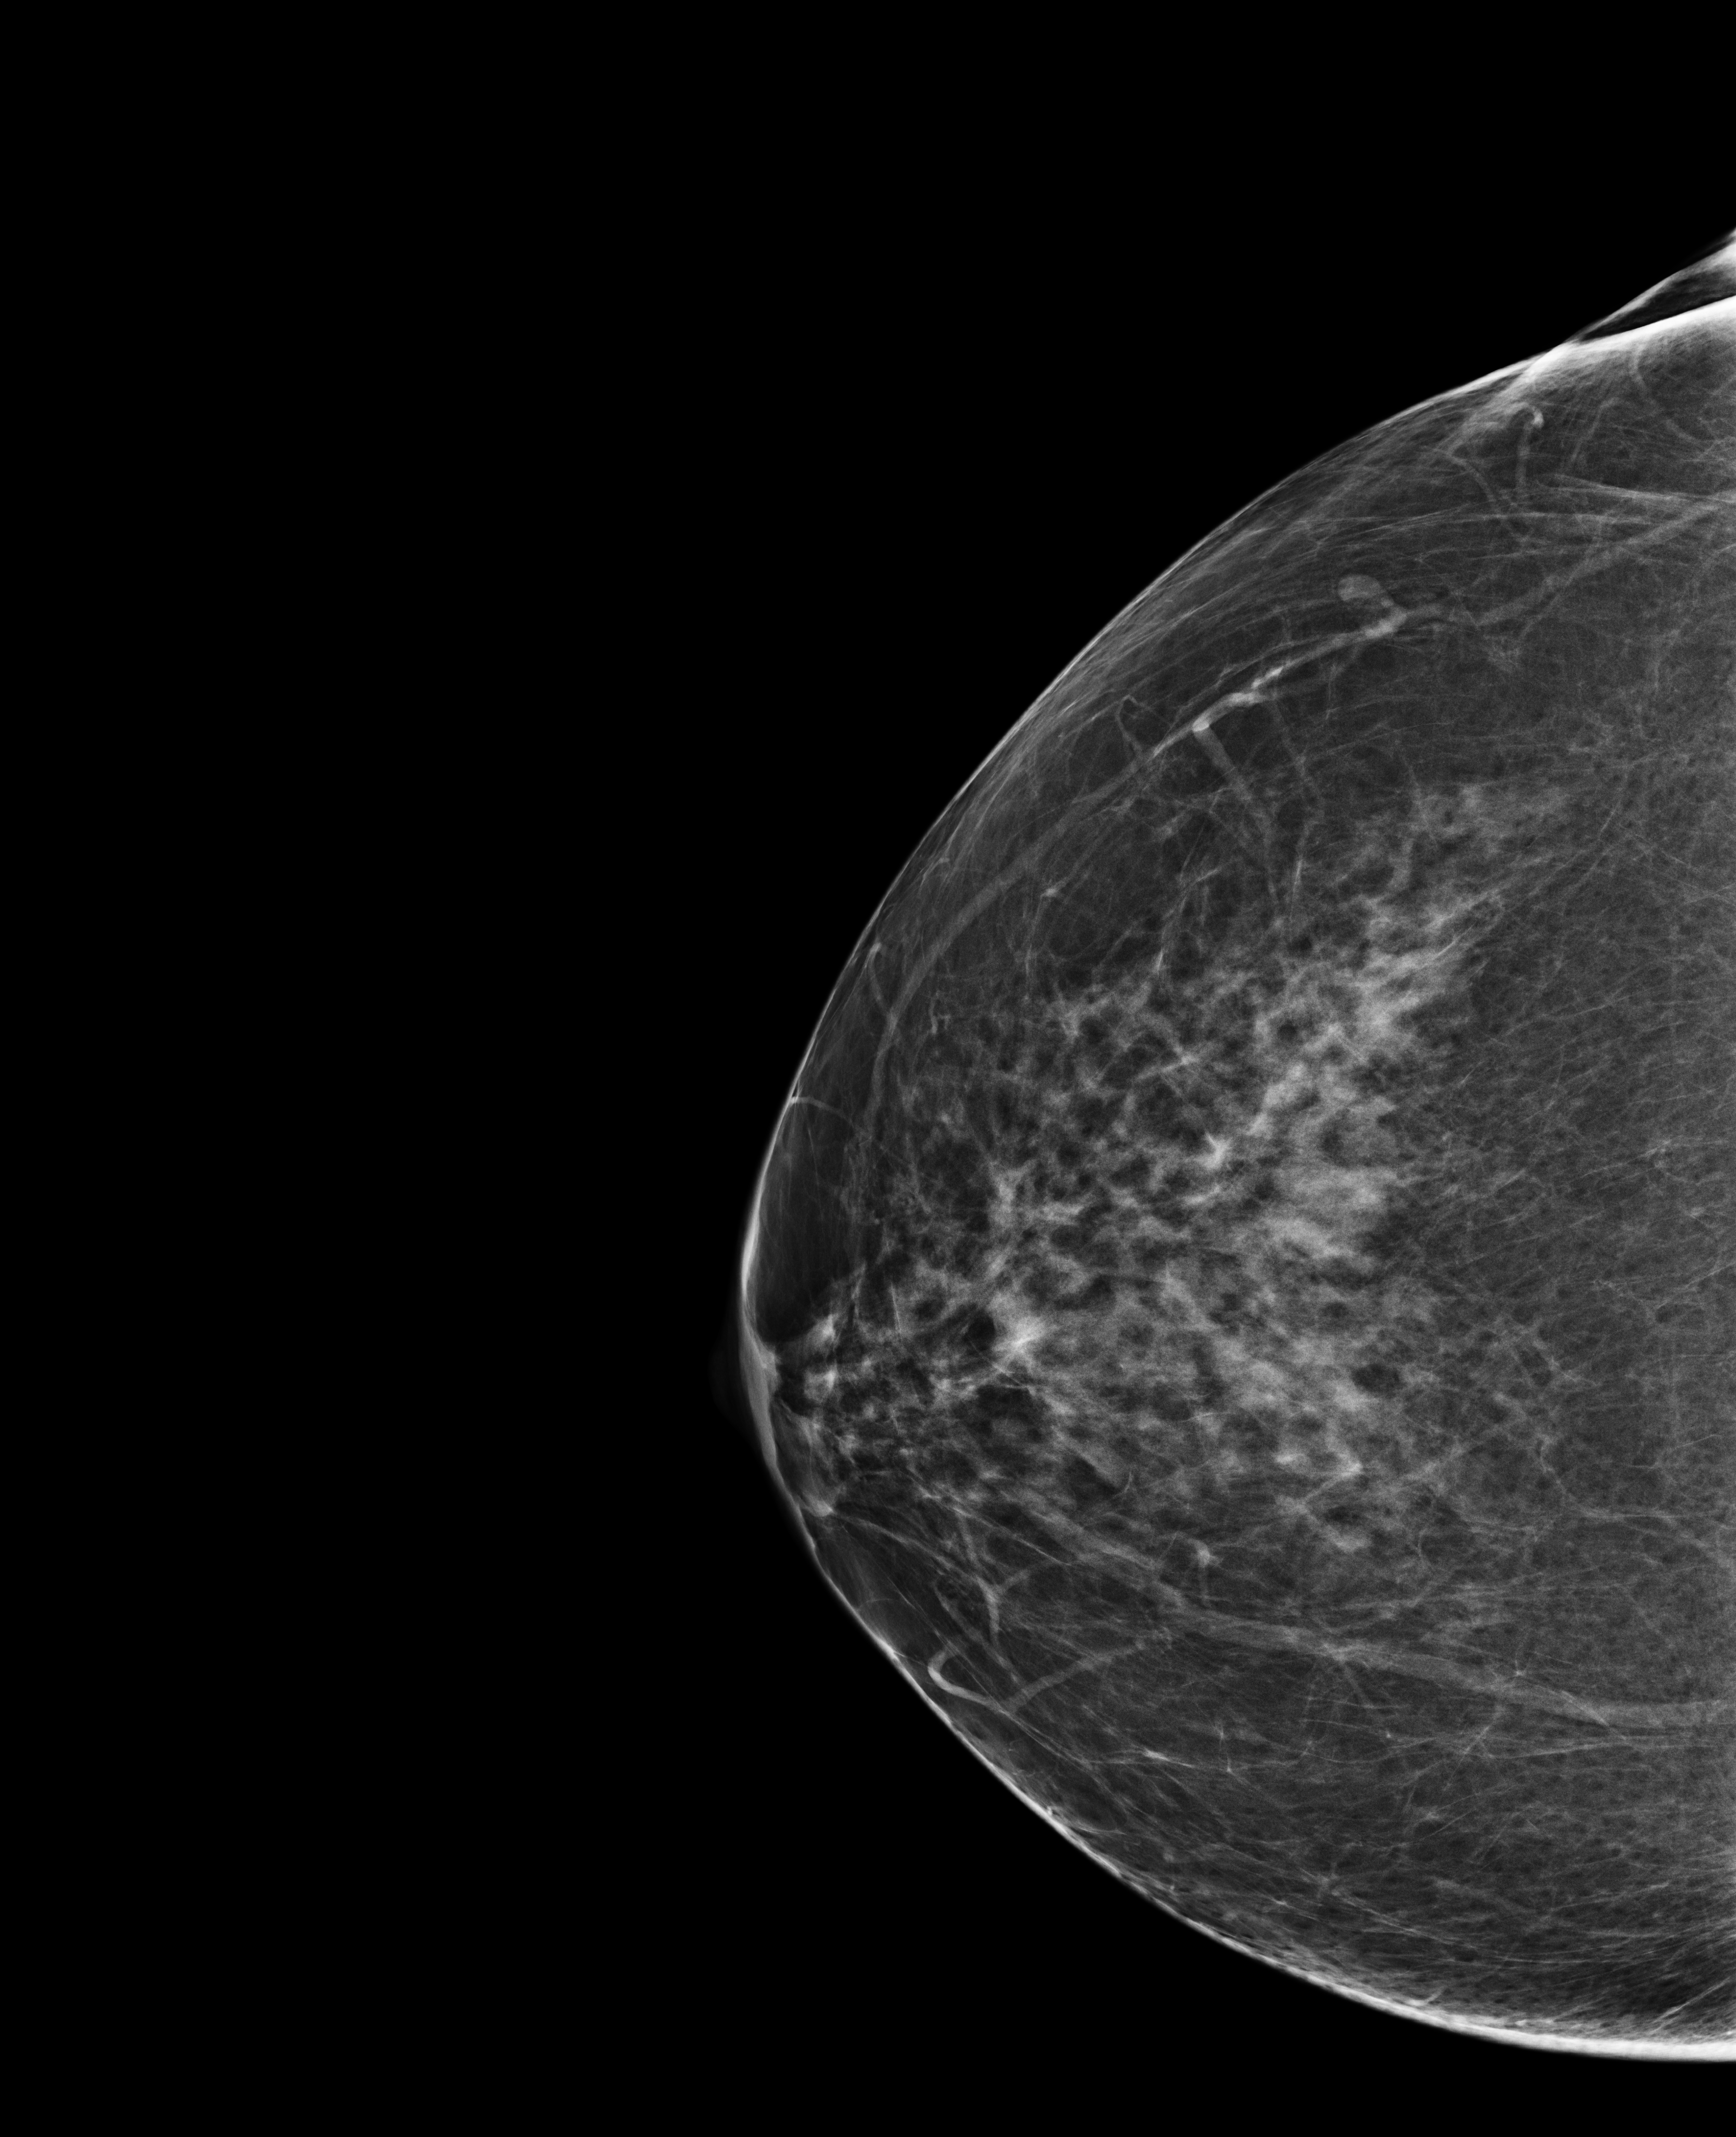
Screening examination; compressed breast thickness 80 mm; system: Selenia Dimensions. Patient: female, 59 years.
Image type: full-field digital mammogram. Breast: right. Projection: cranio-caudal projection. Breast density at the screening exam (both breasts): heterogeneously dense (BI-RADS density category c). Final BI-RADS assessment for this screening round (tomosynthesis exam, both breasts): category 1. Recall: no recall after this screen.